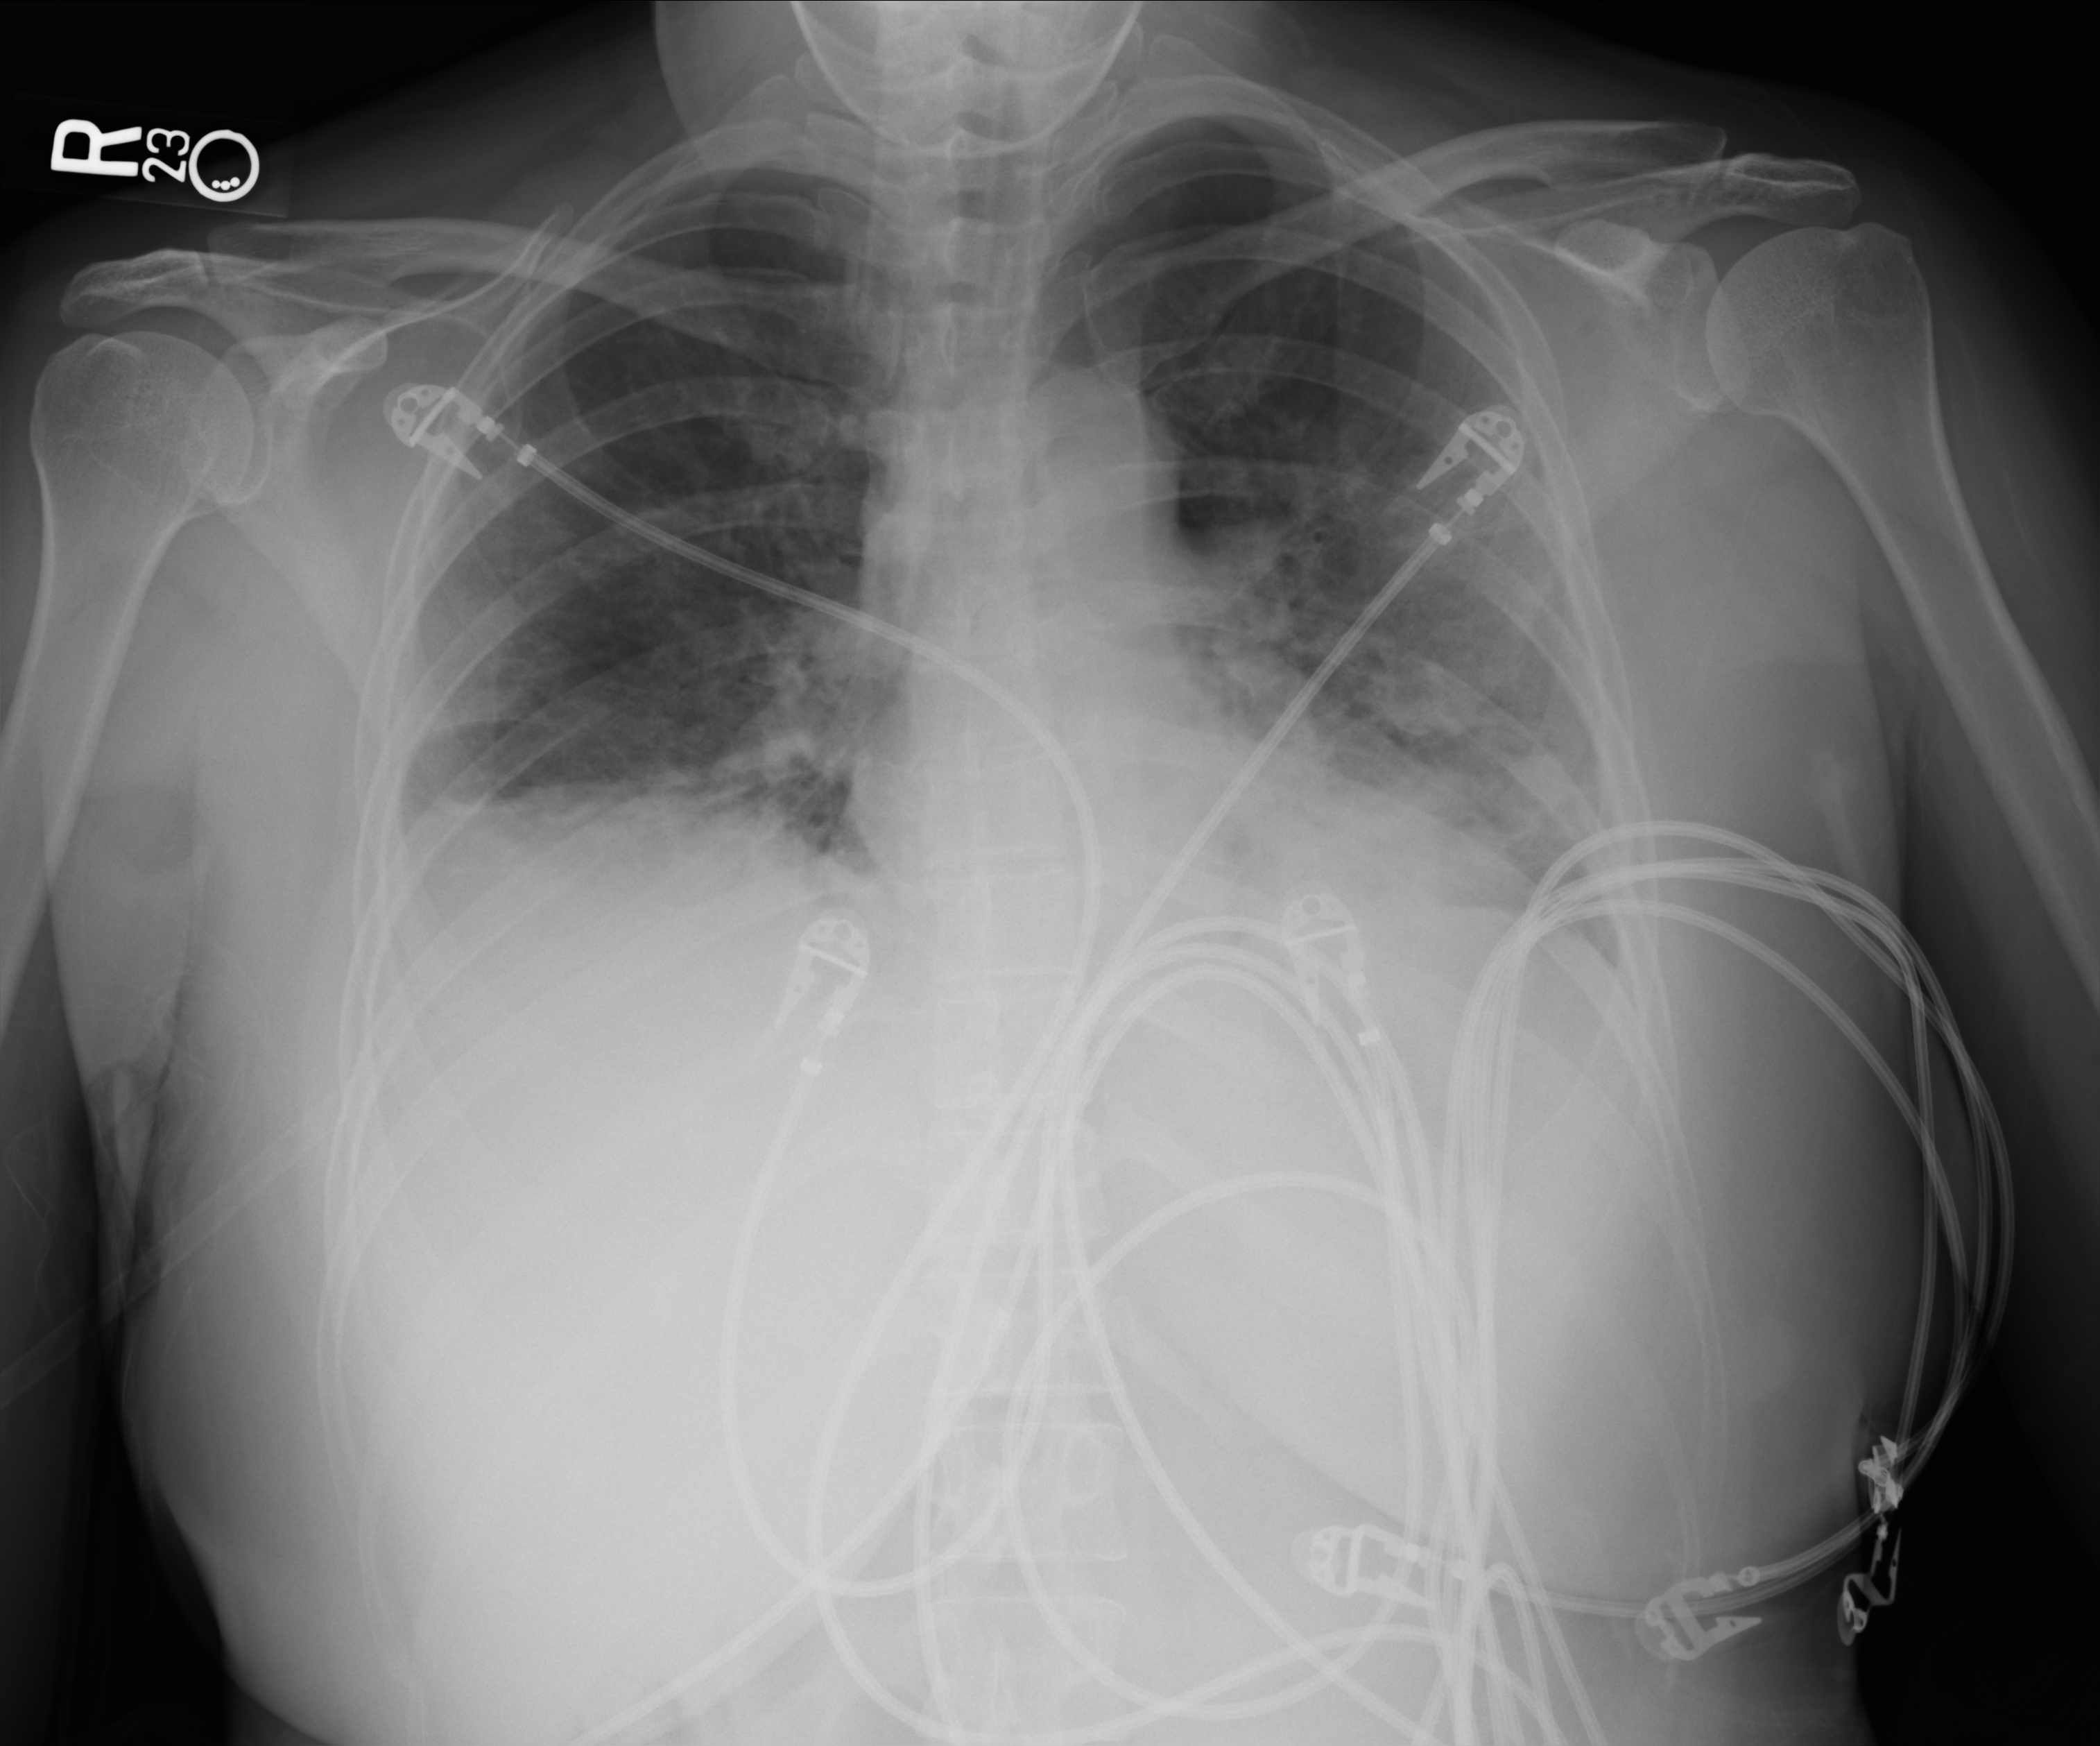
Chest X-ray (portable). Female patient hospitalised with COVID-19, age 18–59 years.
From the hospital-stay record, not from the radiograph (when in the stay this image was taken is not recorded):
- mechanically ventilated during this hospital stay: no